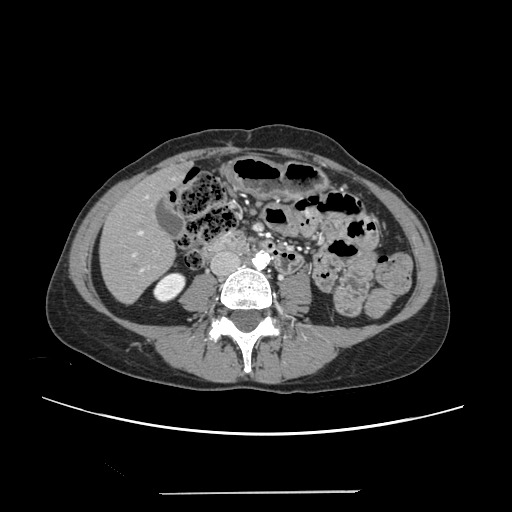
Contrast-enhanced abdominal CT, one axial slice. Slice 64 of 240 in the series (ordered by position). 120 kVp. Intravenous contrast given. Soft-tissue window (W 400 / L 40 HU). 512 × 512 image matrix. Female patient, age 60 years. From the clinical record (not read from this slice): diagnosis: colorectal cancer liver metastases, imaged before liver resection; multiple liver metastases: no; largest metastasis: 1.5 cm; disease in both lobes: no.
Structures marked on this image (outlined manually by an expert reader):
- liver: box from (x=101, y=167) to (x=185, y=302) px
- planned liver remnant (the part of the liver to remain after resection): (x=101, y=171)–(x=175, y=302)
- portal vein (with intrahepatic branches): (x=132, y=195)–(x=159, y=272)